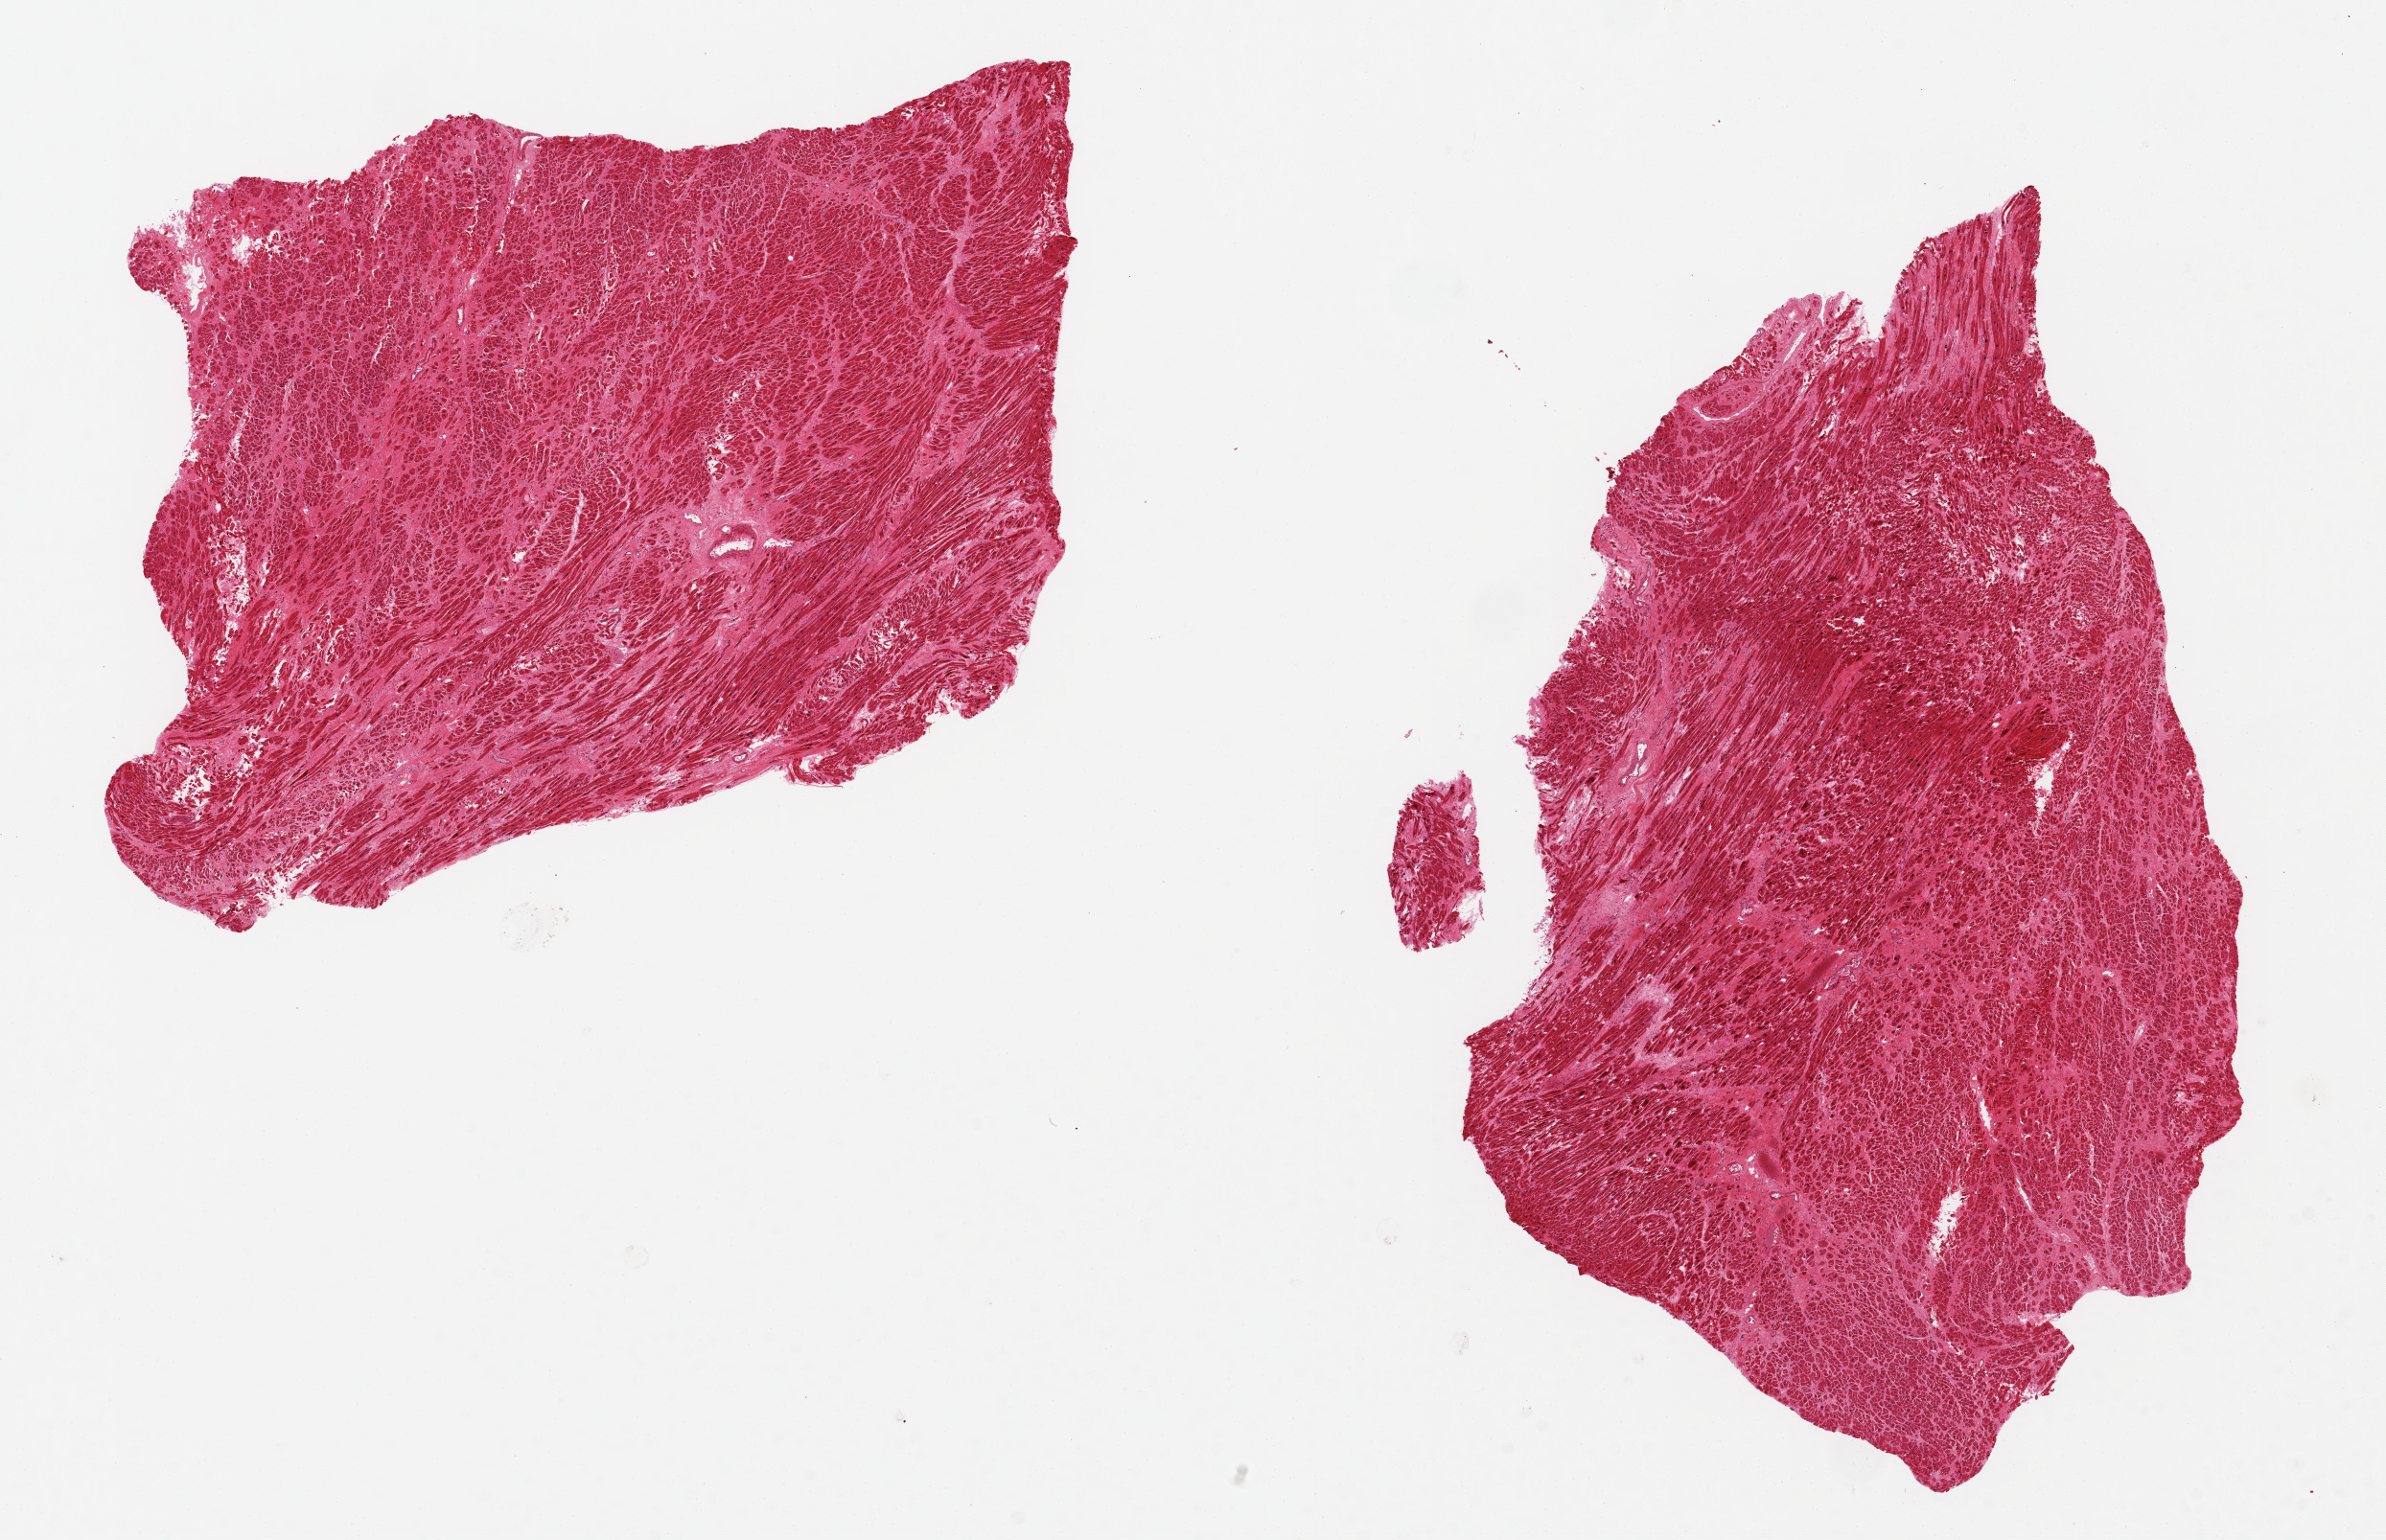
Whole-slide image, H&E stain, shown as a low-resolution overview of the whole scanned area (about 19.7 x 12.7 mm, from a 20x scan), PAXgene-fixed, paraffin-embedded tissue, section of heart (target tissue), tissue donor sample. Female donor.
Pathologist's review note for this sample: 2 pieces 9x7 & 8x5 mm; moderate diffuse interstitial fibrosis; hypertrophied nuclei.